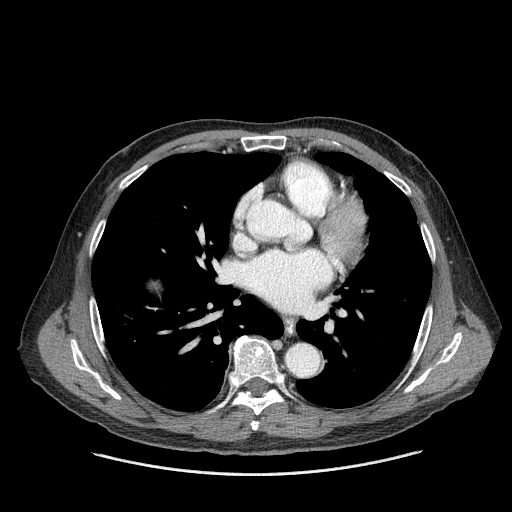
Contrast-enhanced abdominal CT (liver protocol), one axial slice; position 170 of 180 along the scan axis; reconstruction kernel STANDARD; one of 2 acquisitions stored at this slice position; soft-tissue window (W 400 / L 40 HU); 2.5 mm slice thickness; 512 × 512 image matrix, field of view 420 × 420 mm. Case-level facts recorded for this patient, not image findings: diagnosis: hepatocellular carcinoma (patient treated with transarterial chemoembolisation; whether this scan precedes or follows treatment is not stated here); TNM stage (as recorded): Stage-II; Child-Pugh class: A; tumour differentiation: well differentiated; tumour nodularity: multinodular.
Annotated regions visible in this slice (semi-automatically segmented with operator editing):
- liver parenchyma outside the tumour (the mass and vessels are separate outlines, so this box may not span the whole liver): box from (x=152, y=282) to (x=158, y=288) px